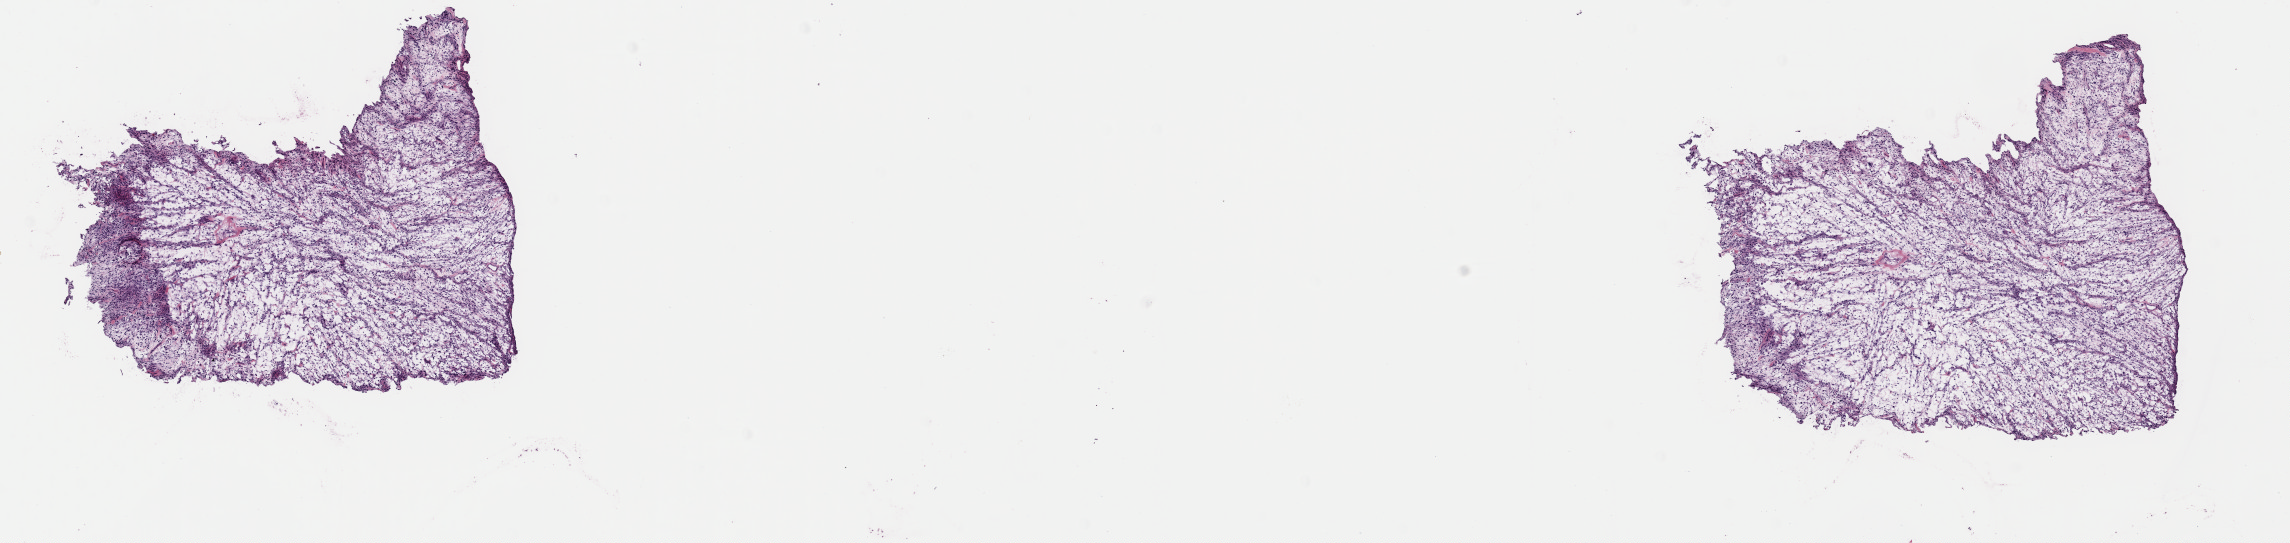
Whole-slide histology image, H&E-stained — shown as a low-resolution overview of the whole scanned area (about 18.1 x 4.3 mm, acquisition: 40x scan). Frozen section from the top of the tissue portion. Sample: primary tumour, retroperitoneum and peritoneum. Male patient; age at initial diagnosis 47 years.
Histologic diagnosis: Dedifferentiated liposarcoma (retroperitoneum).